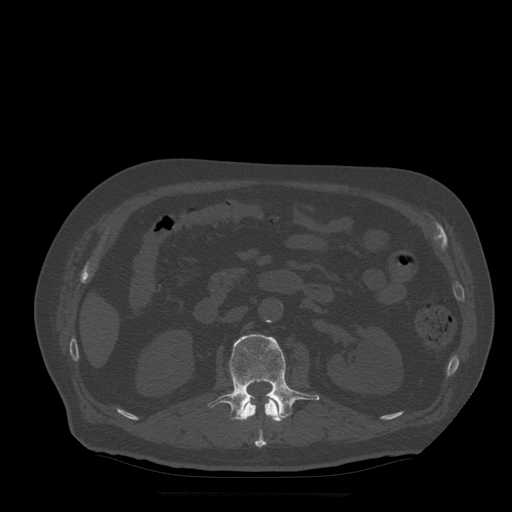
CT including the spine, one axial slice. Slice 175 of 522 in the series (ordered by position). Bone window (W 1800 / L 400 HU). 1.25 mm slice thickness. 512 × 512 image matrix. Patient age 72 years. From the clinical record (not read from this slice): primary cancer: prostate.
Annotated regions visible in this slice (semi-automatic segmentation, software-assisted and operator-edited):
- L1 vertebra: box from (x=241, y=396) to (x=281, y=448) px
- L2 vertebra: (x=208, y=334)–(x=320, y=420)